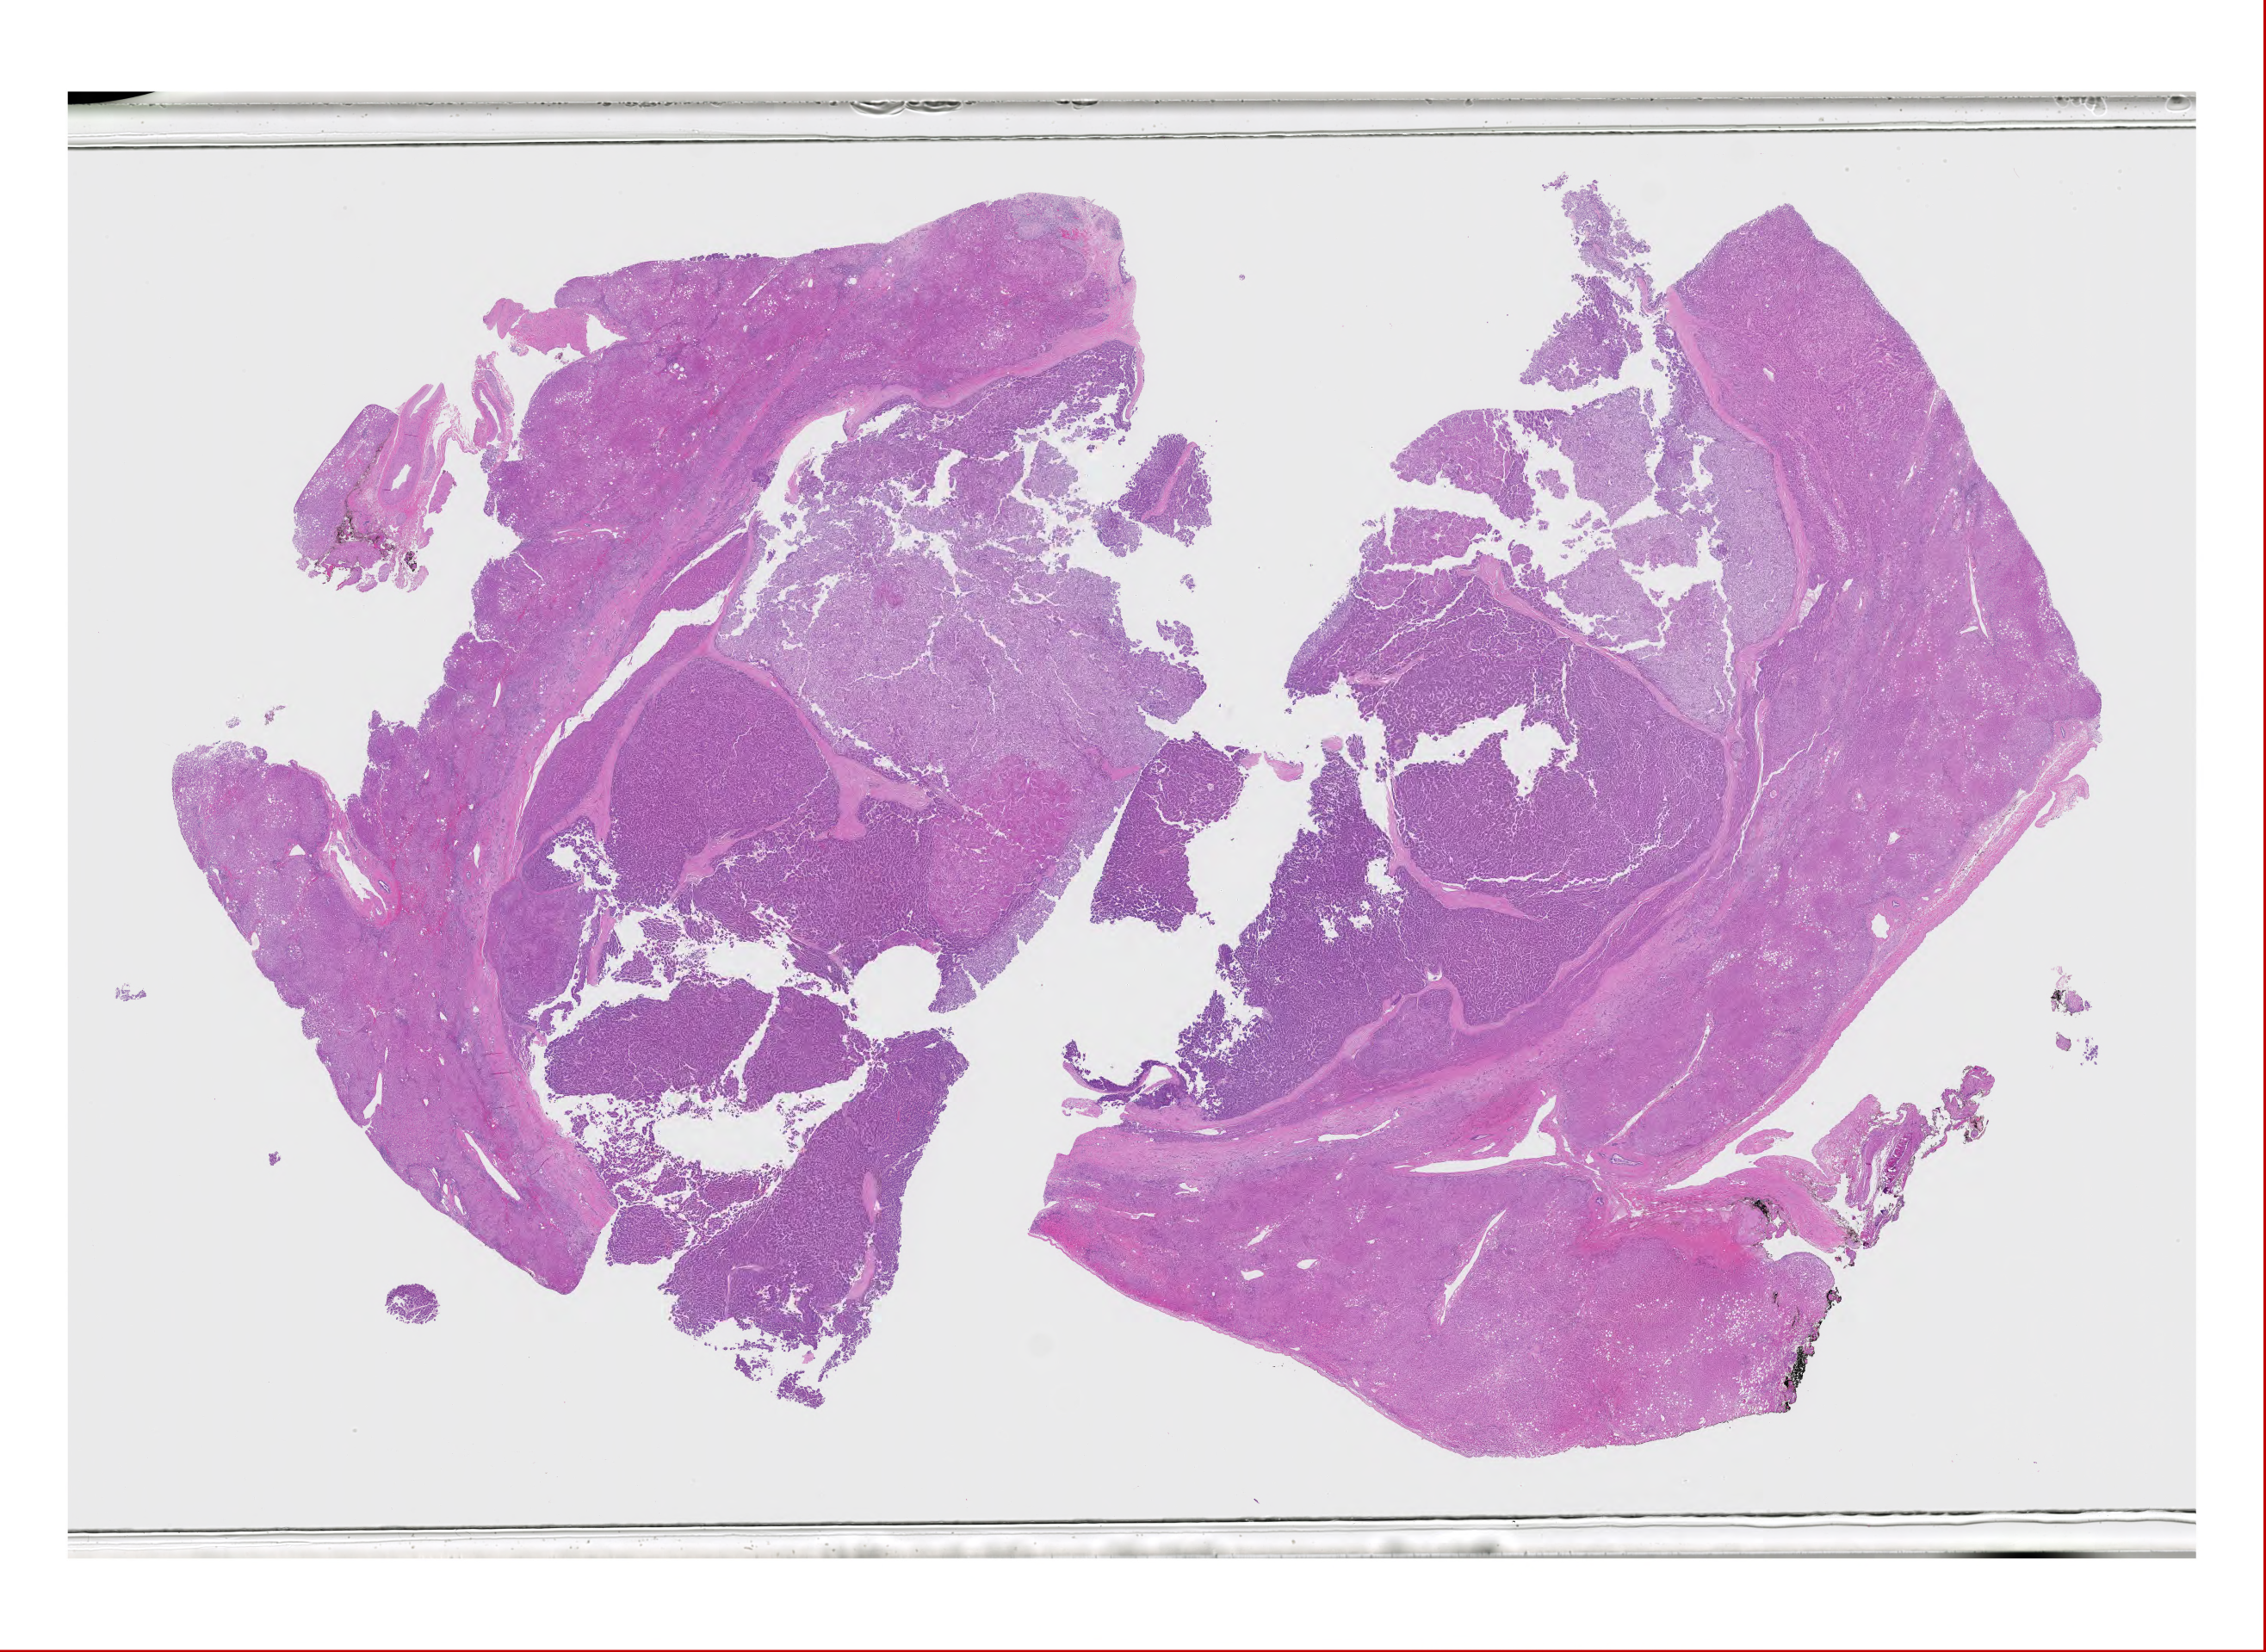
Whole-slide histology image, Hematoxylin and eosin (H&E) stained — whole scanned area (about 42.1 x 30.7 mm, acquisition: 20x scan) shown as a low-resolution overview; formalin-fixed paraffin-embedded (FFPE) diagnostic section; sample: primary tumour, liver. Patient: male, age at initial diagnosis 71 years. Histologic grade: G2 (moderately differentiated).
Pathologic diagnosis: Hepatocellular carcinoma, NOS. AJCC pathologic stage: I.